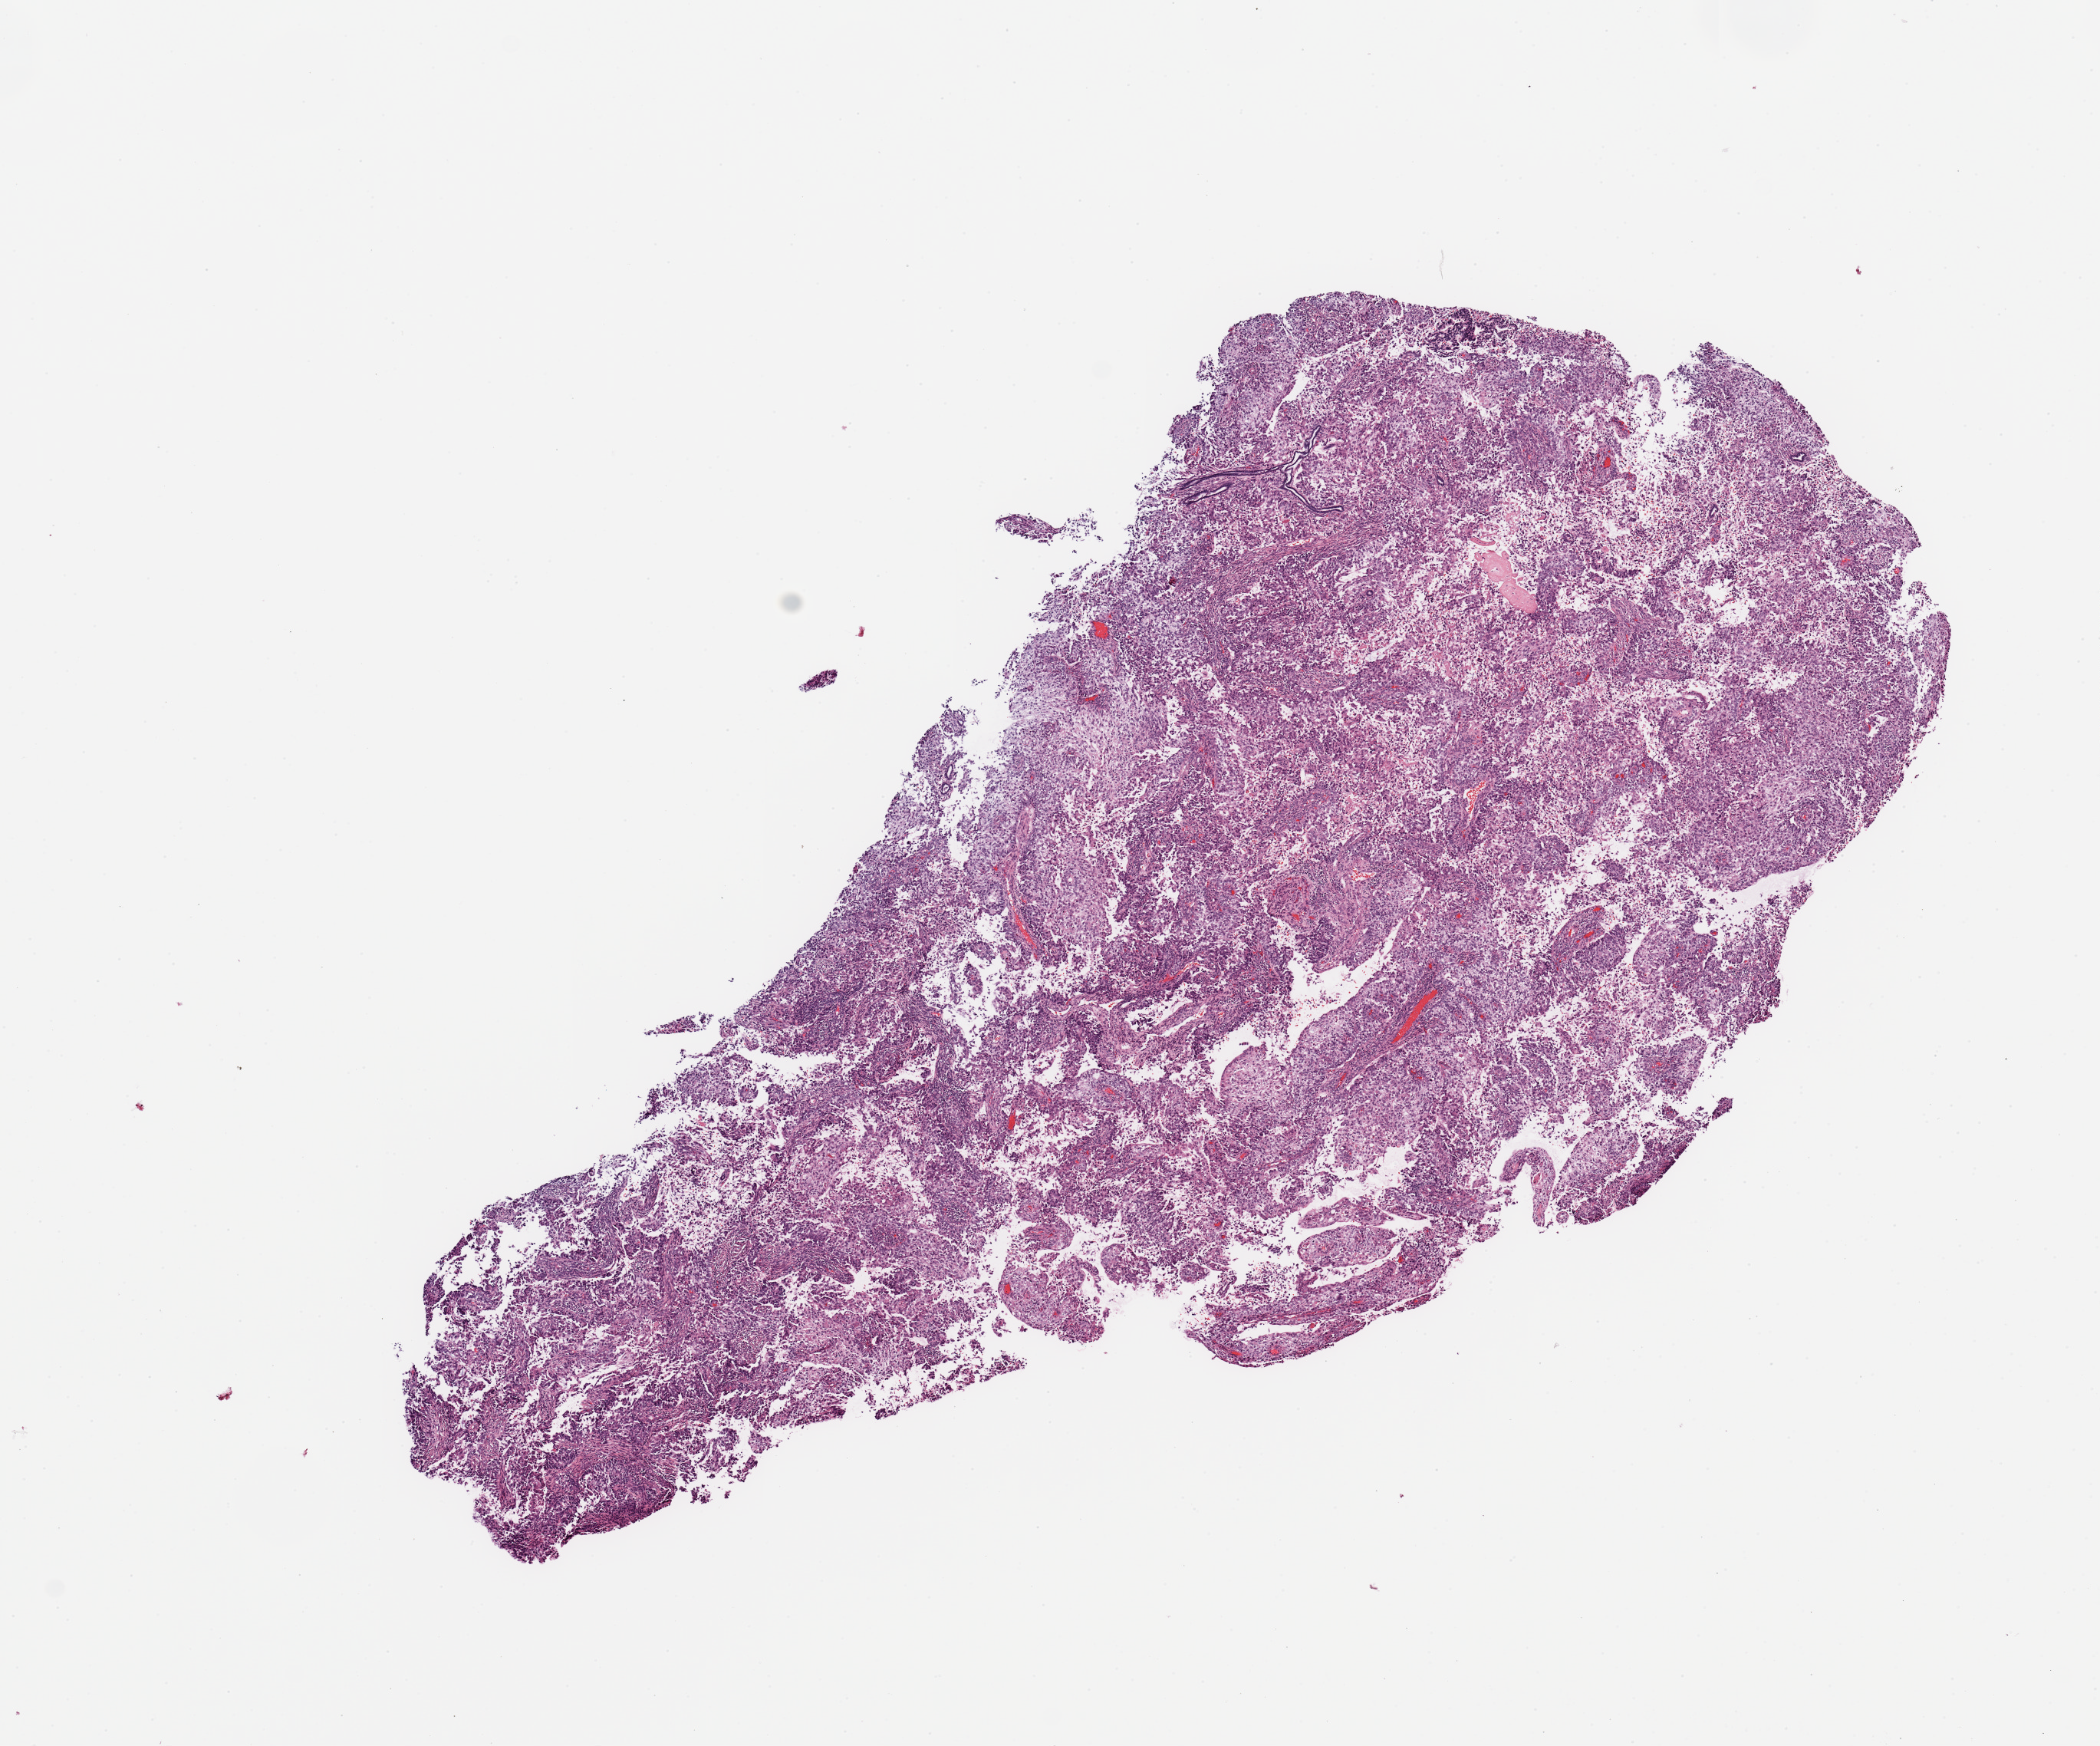
Digitized Hematoxylin and eosin (H&E) stained tissue section (whole slide) — a low-resolution overview of the entire scanned area, about 10.8 x 9.0 mm (acquisition: 20x scan); tumour tissue sample, sampled site: uterus. Female, 64 y/o. Histologic grade: G3 (poorly differentiated). Pathologist review of this section (percent, as recorded): tumour nuclei 95%, necrosis 0%.
- AJCC pathologic stage: III
- diagnosis: Endometrioid adenocarcinoma, NOS